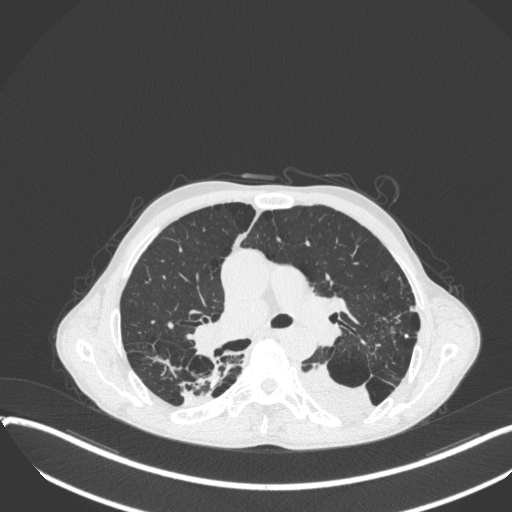
Chest CT, one axial slice; slice 234 of 400 in the series (ordered by position); 120 kVp; lung window (W 1500 / L -600 HU); 1 mm slice thickness; 512 × 512 image matrix, field of view 400 × 400 mm. Male patient, age 57 years. Case-level facts recorded for this patient, not image findings: clinical TNM (as recorded): T4 N0 M0.
Annotated regions visible in this slice (bounding box drawn by a radiologist):
- lung tumour (recorded histology: squamous cell carcinoma): bounding box (x1, y1, x2, y2) in pixels: (295, 353, 382, 421)